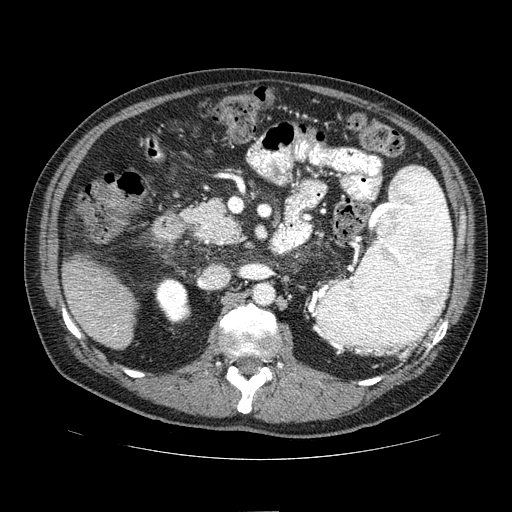
Contrast-enhanced abdominal CT (liver protocol), one axial slice; position 24 of 81 along the scan axis; one of 2 acquisitions stored at this slice position; soft-tissue window (W 400 / L 40 HU); 2.5 mm slice thickness; 512 × 512 image matrix. From the clinical record (not read from this slice): diagnosis: hepatocellular carcinoma (patient treated with transarterial chemoembolisation; whether this scan precedes or follows treatment is not stated here); TNM stage (as recorded): Stage-IIIA; Child-Pugh class: A; tumour differentiation: well differentiated; tumour size: 5.6 cm.
Annotated regions visible in this slice (semi-automatically segmented with operator editing):
- liver parenchyma outside the tumour (the mass and vessels are separate outlines, so this box may not span the whole liver): box from (x=62, y=256) to (x=137, y=350) px
- liver vessels: (x=87, y=305)–(x=117, y=335)